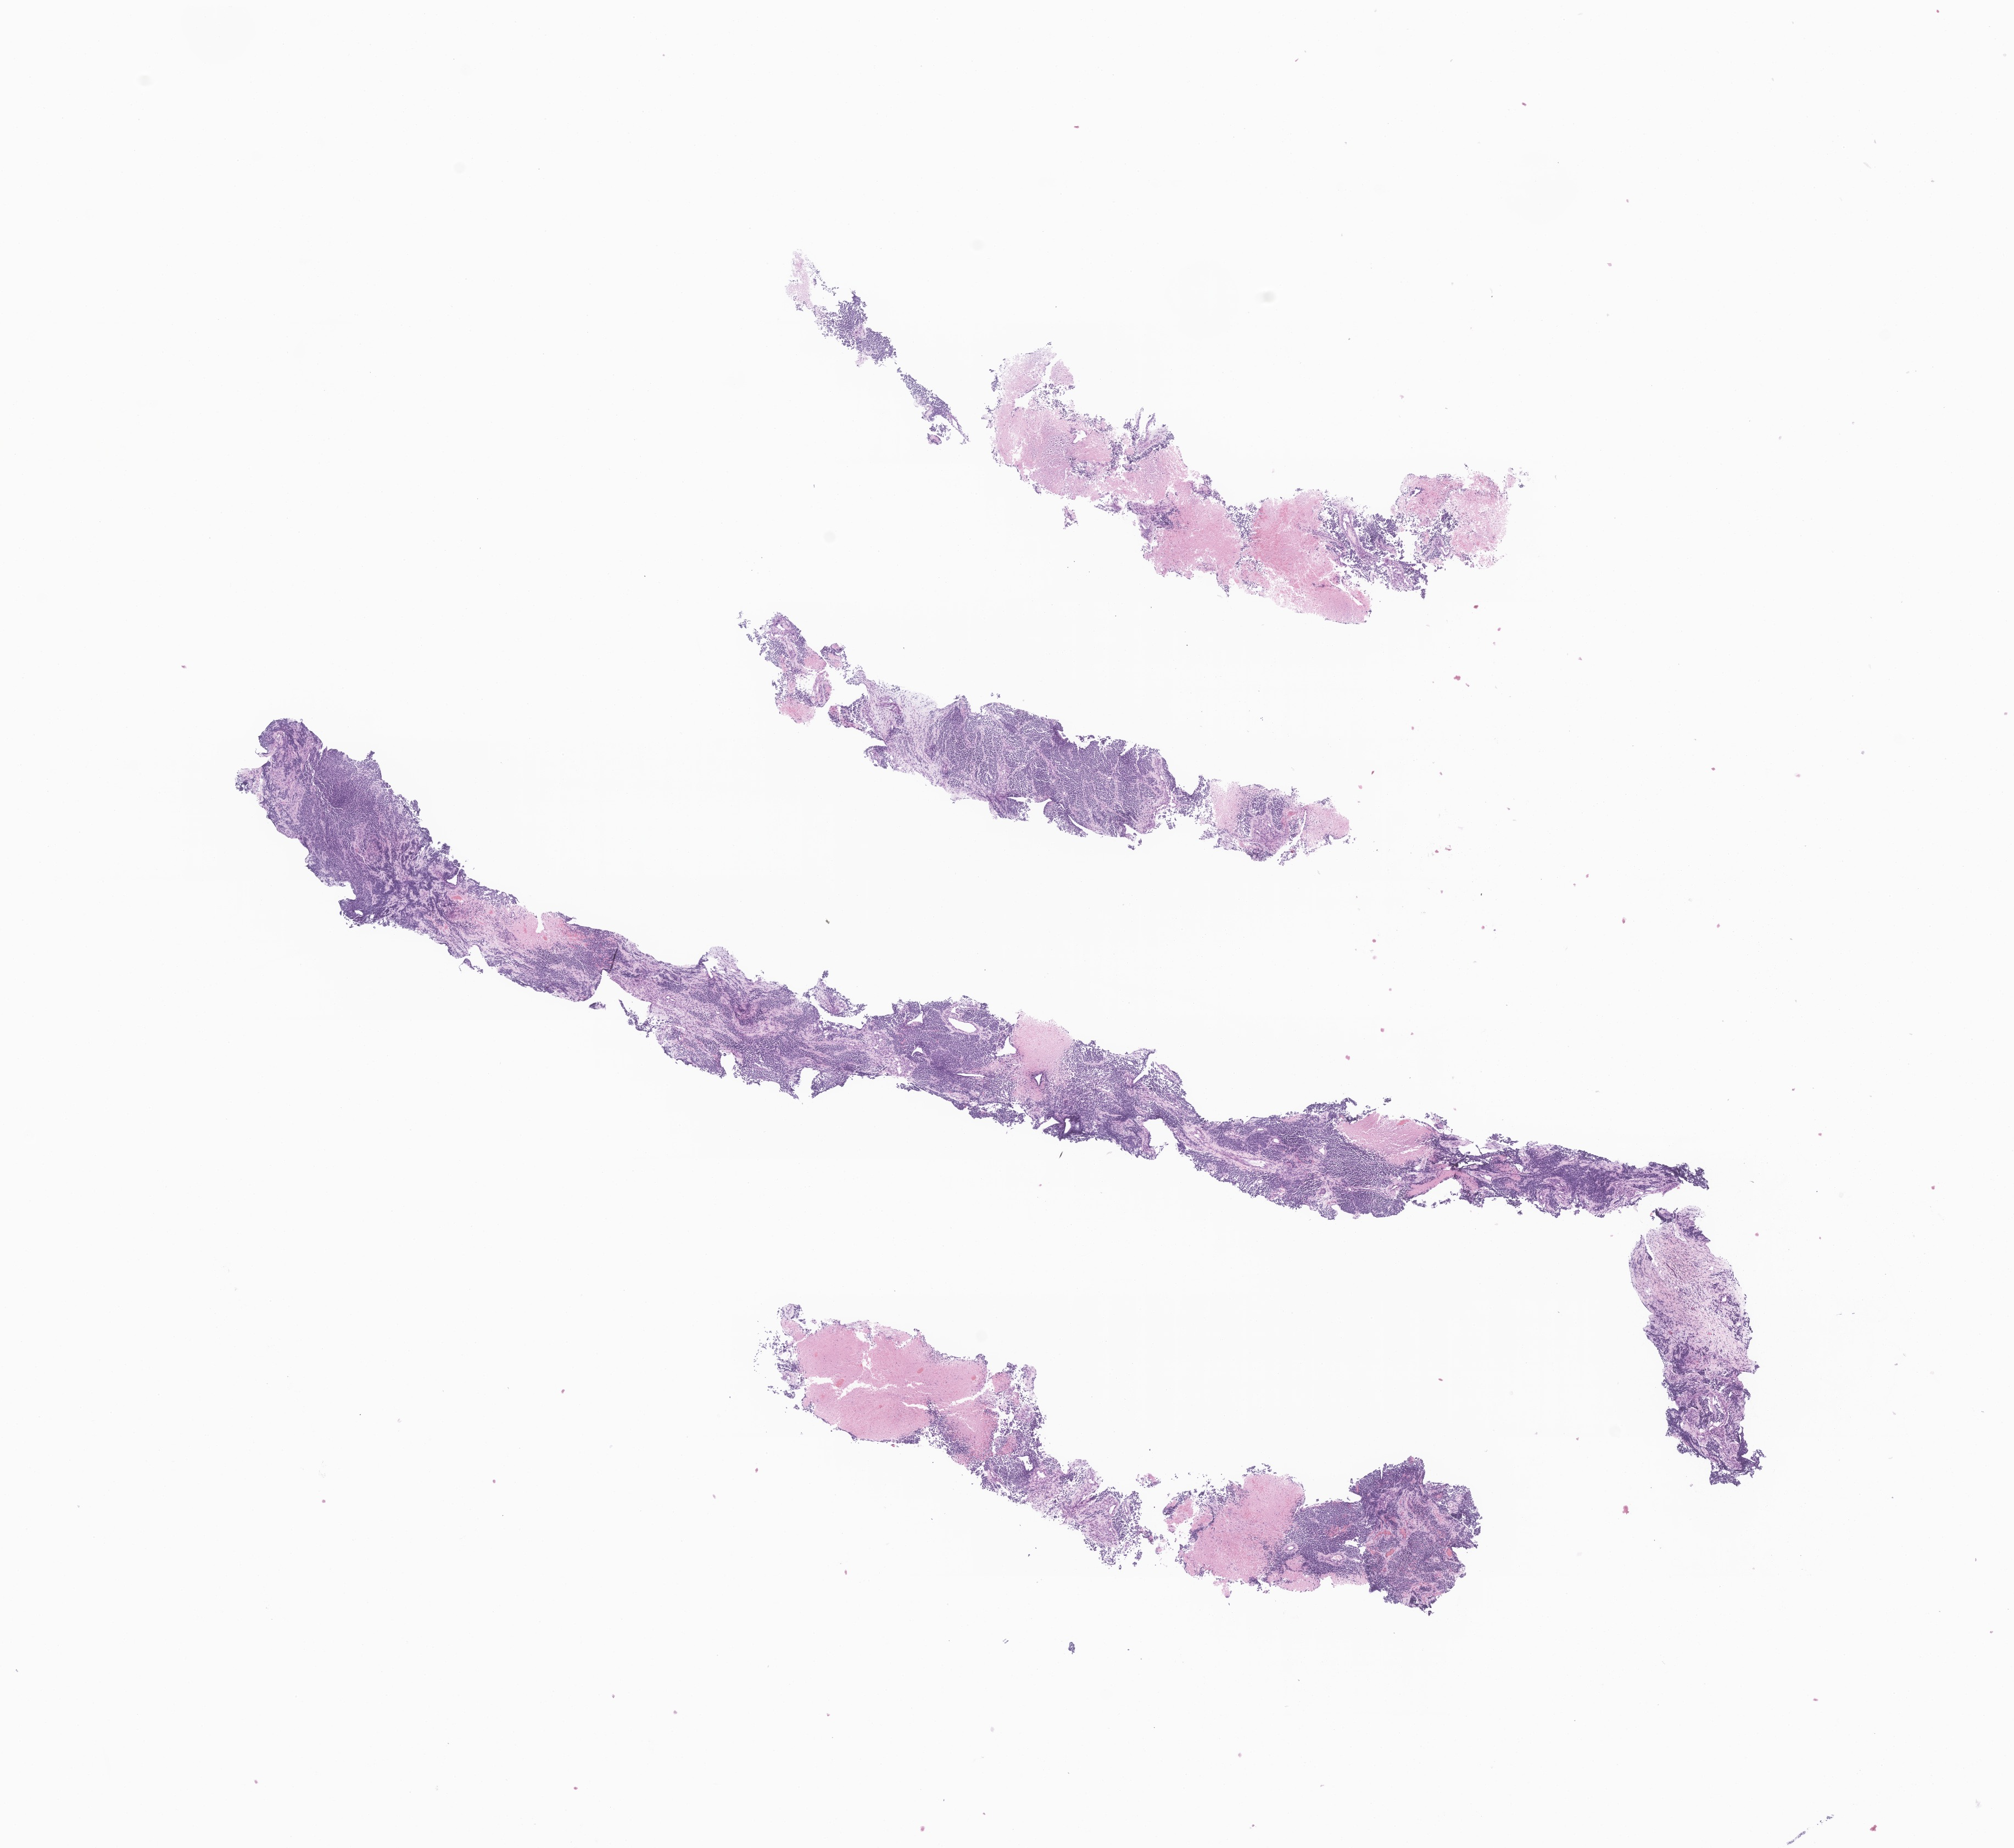
Hematoxylin and eosin (H&E) whole-slide image of tumor tissue from the retroperitoneum — shown as a low-resolution overview of the whole scanned area (about 15.5 x 14.2 mm); formalin-fixed paraffin-embedded section. Female patient, age 65 months (5 years 5 months).
Diagnosis: Neuroblastoma, NOS.